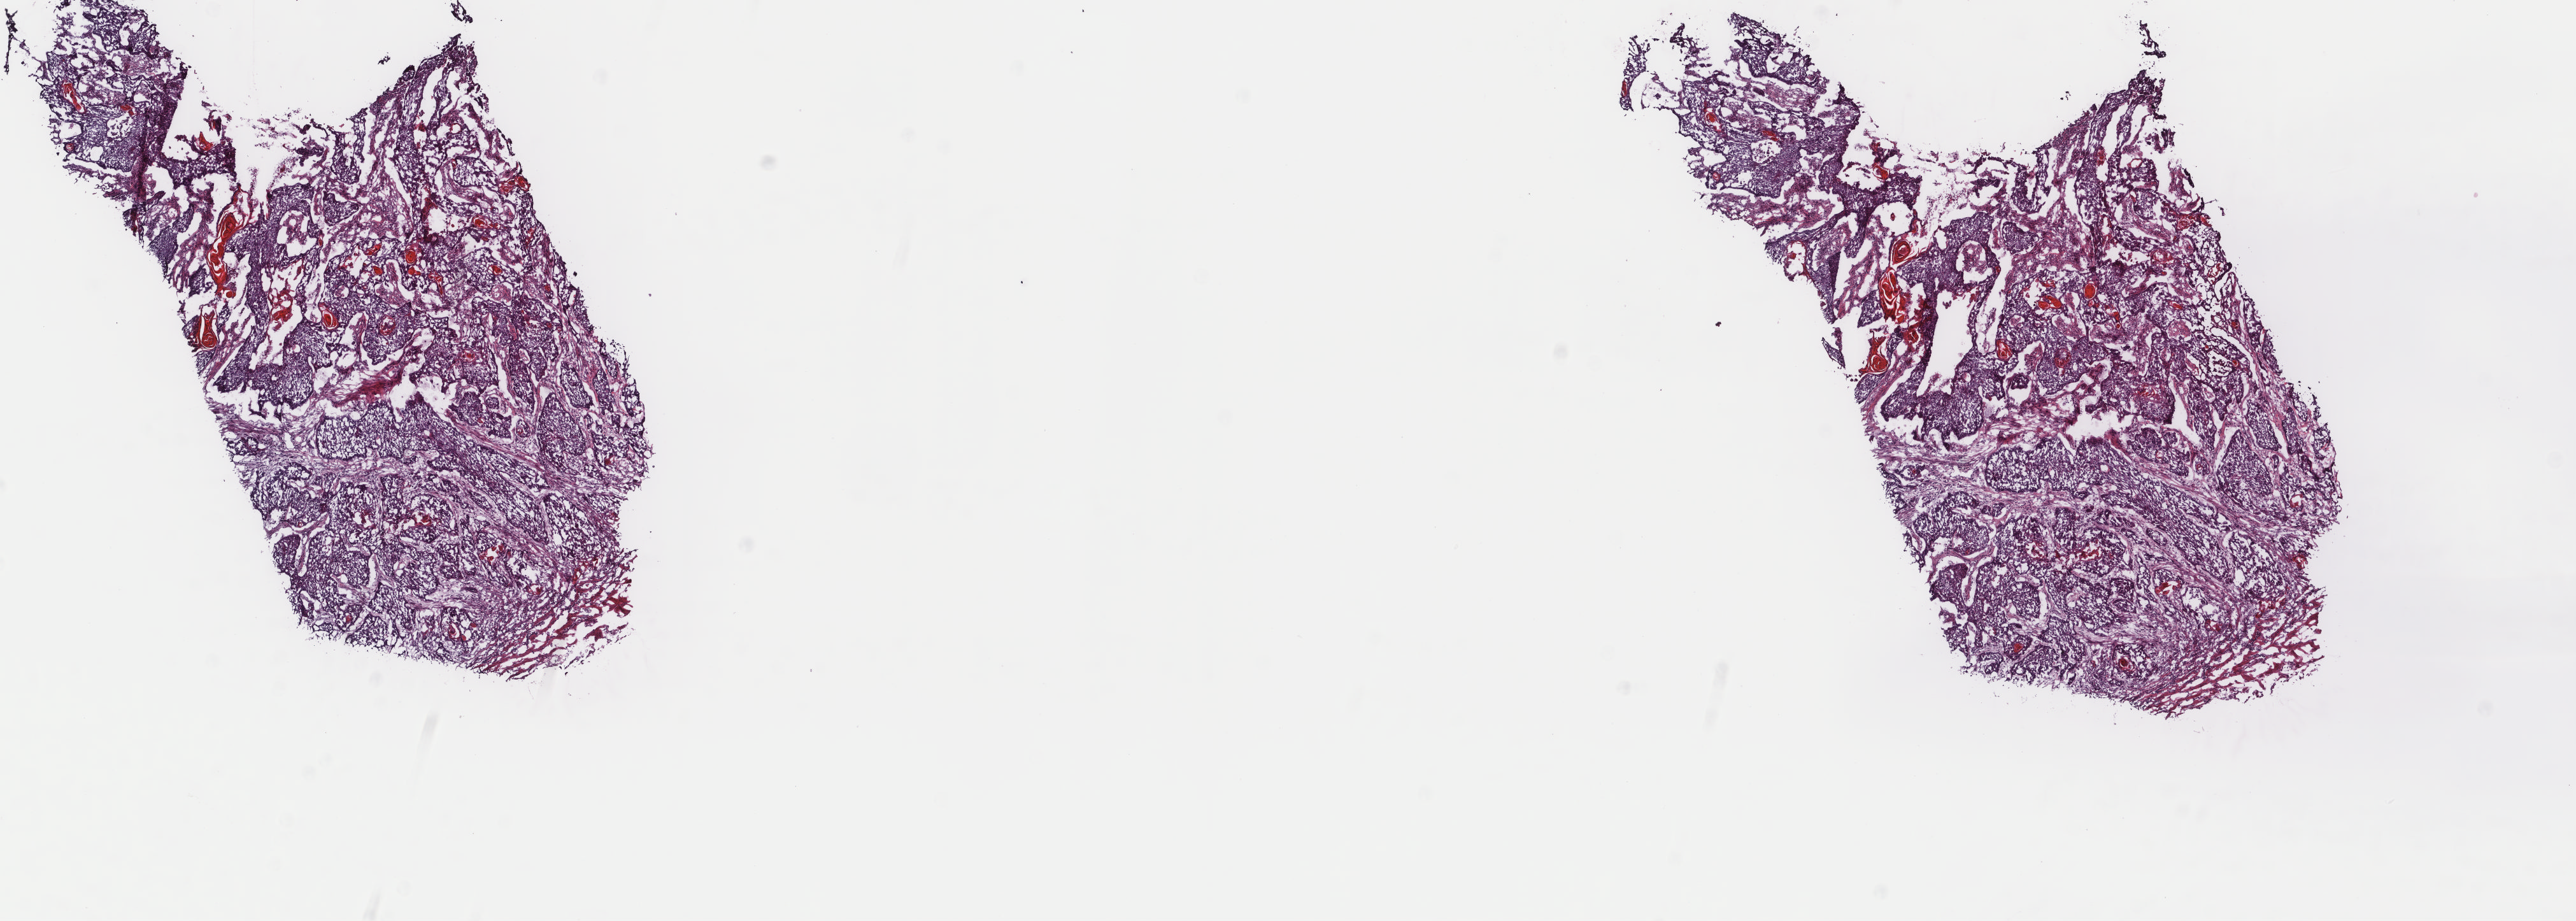
H&E-stained whole-slide image, whole scanned area (about 16.1 x 5.7 mm, acquisition: 40x scan) shown as a low-resolution overview; frozen section; sample: primary tumour, esophagus. Male patient; age at initial diagnosis 54 years. Composition of this section per pathologist review: tumour cells 80%, tumour nuclei 100%.
Pathologic diagnosis: Squamous cell carcinoma, keratinizing, NOS (lower third of esophagus).